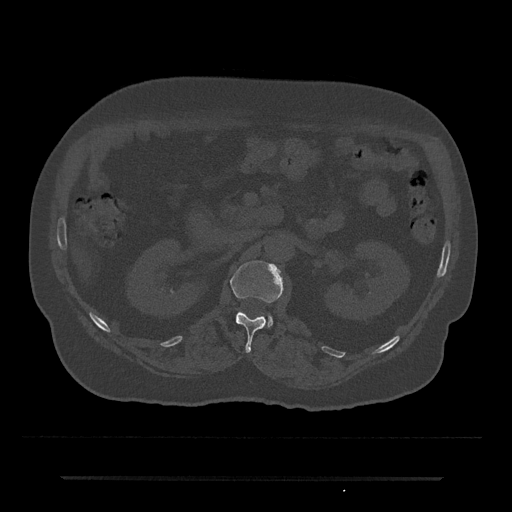
CT including the spine, one axial slice; slice 58 of 797 in the series (ordered by position); 120 kVp; bone window (W 1800 / L 400 HU); 0.5 mm slice thickness; 512 × 512 image matrix. Patient: male, 69 years. Case-level facts recorded for this patient, not image findings: primary cancer: prostate.
Structures marked on this image (semi-automatic segmentation, software-assisted and operator-edited):
- L1 vertebra: bounding box (x1, y1, x2, y2) in pixels: (230, 261, 283, 353)
- L2 vertebra: (268, 316, 273, 326)